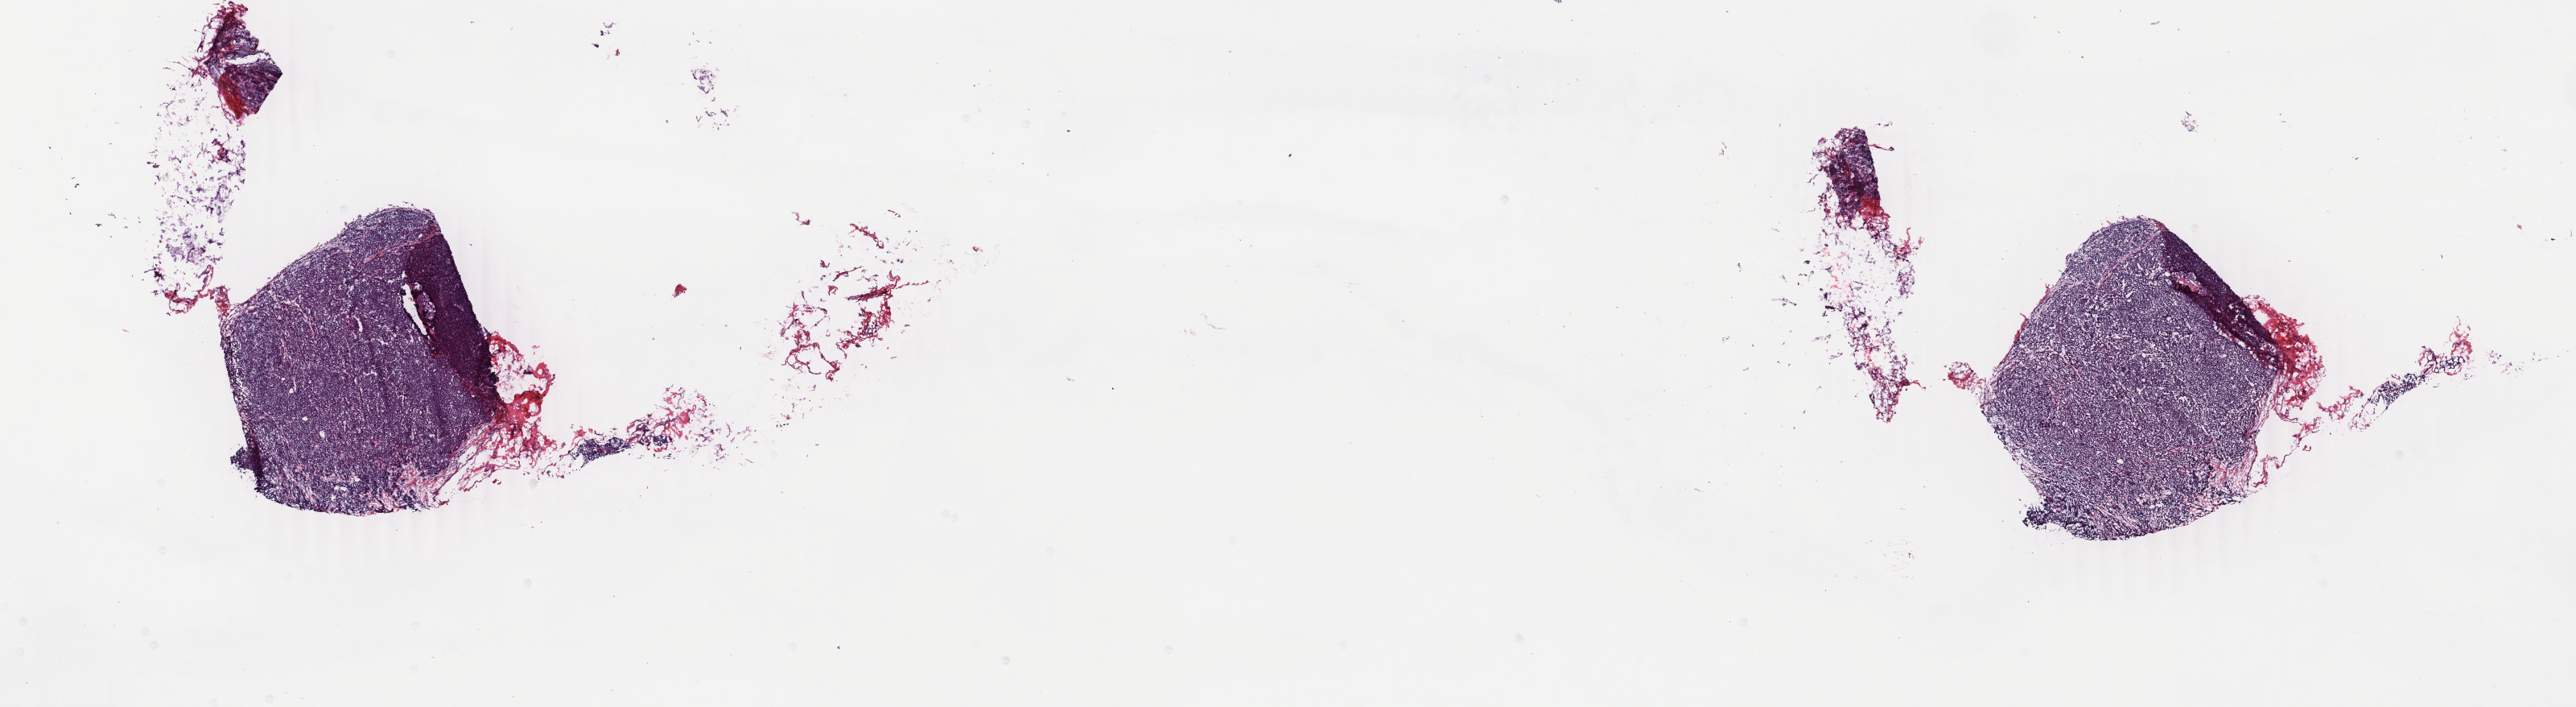
Hematoxylin and eosin (H&E) stained whole-slide image, shown as a low-resolution overview of the whole scanned area (about 25.5 x 7.0 mm, acquisition: 40x scan); frozen section; primary tumour sample from the breast. Female patient; age at initial diagnosis 58 years. Slide review estimates, as recorded: tumour cells 84%, tumour nuclei 90%, normal cells 15%, stromal cells 0%, necrosis 1%. Infiltration values recorded for this section: lymphocyte infiltration 7%, monocyte infiltration 0%, neutrophil infiltration 0%.
• laterality: right
• AJCC pathologic stage: IIIA
• pathologic diagnosis: Infiltrating duct carcinoma, NOS
• lymph nodes positive (case pathology): 5 of 15 examined